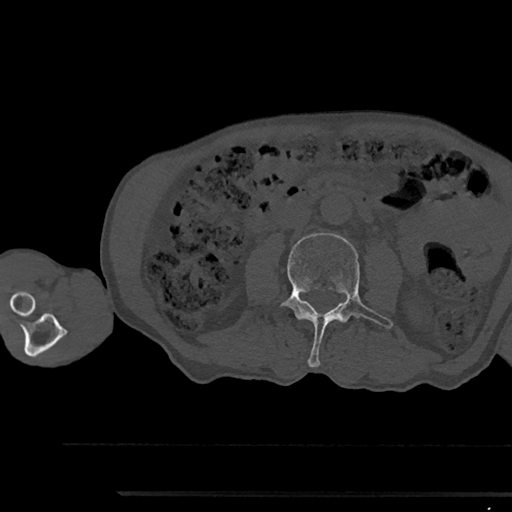
CT including the spine, one axial slice; position 490 of 797 along the scan axis; bone window (W 1800 / L 400 HU); 0.5 mm slice thickness; 512 × 512 image matrix. Patient: male, 79 years. From the clinical record (not read from this slice): primary cancer: prostate.
Structures marked on this image (semi-automatically segmented with operator editing):
- L3 vertebra: bounding box (x1, y1, x2, y2) in pixels: (282, 233, 393, 367)